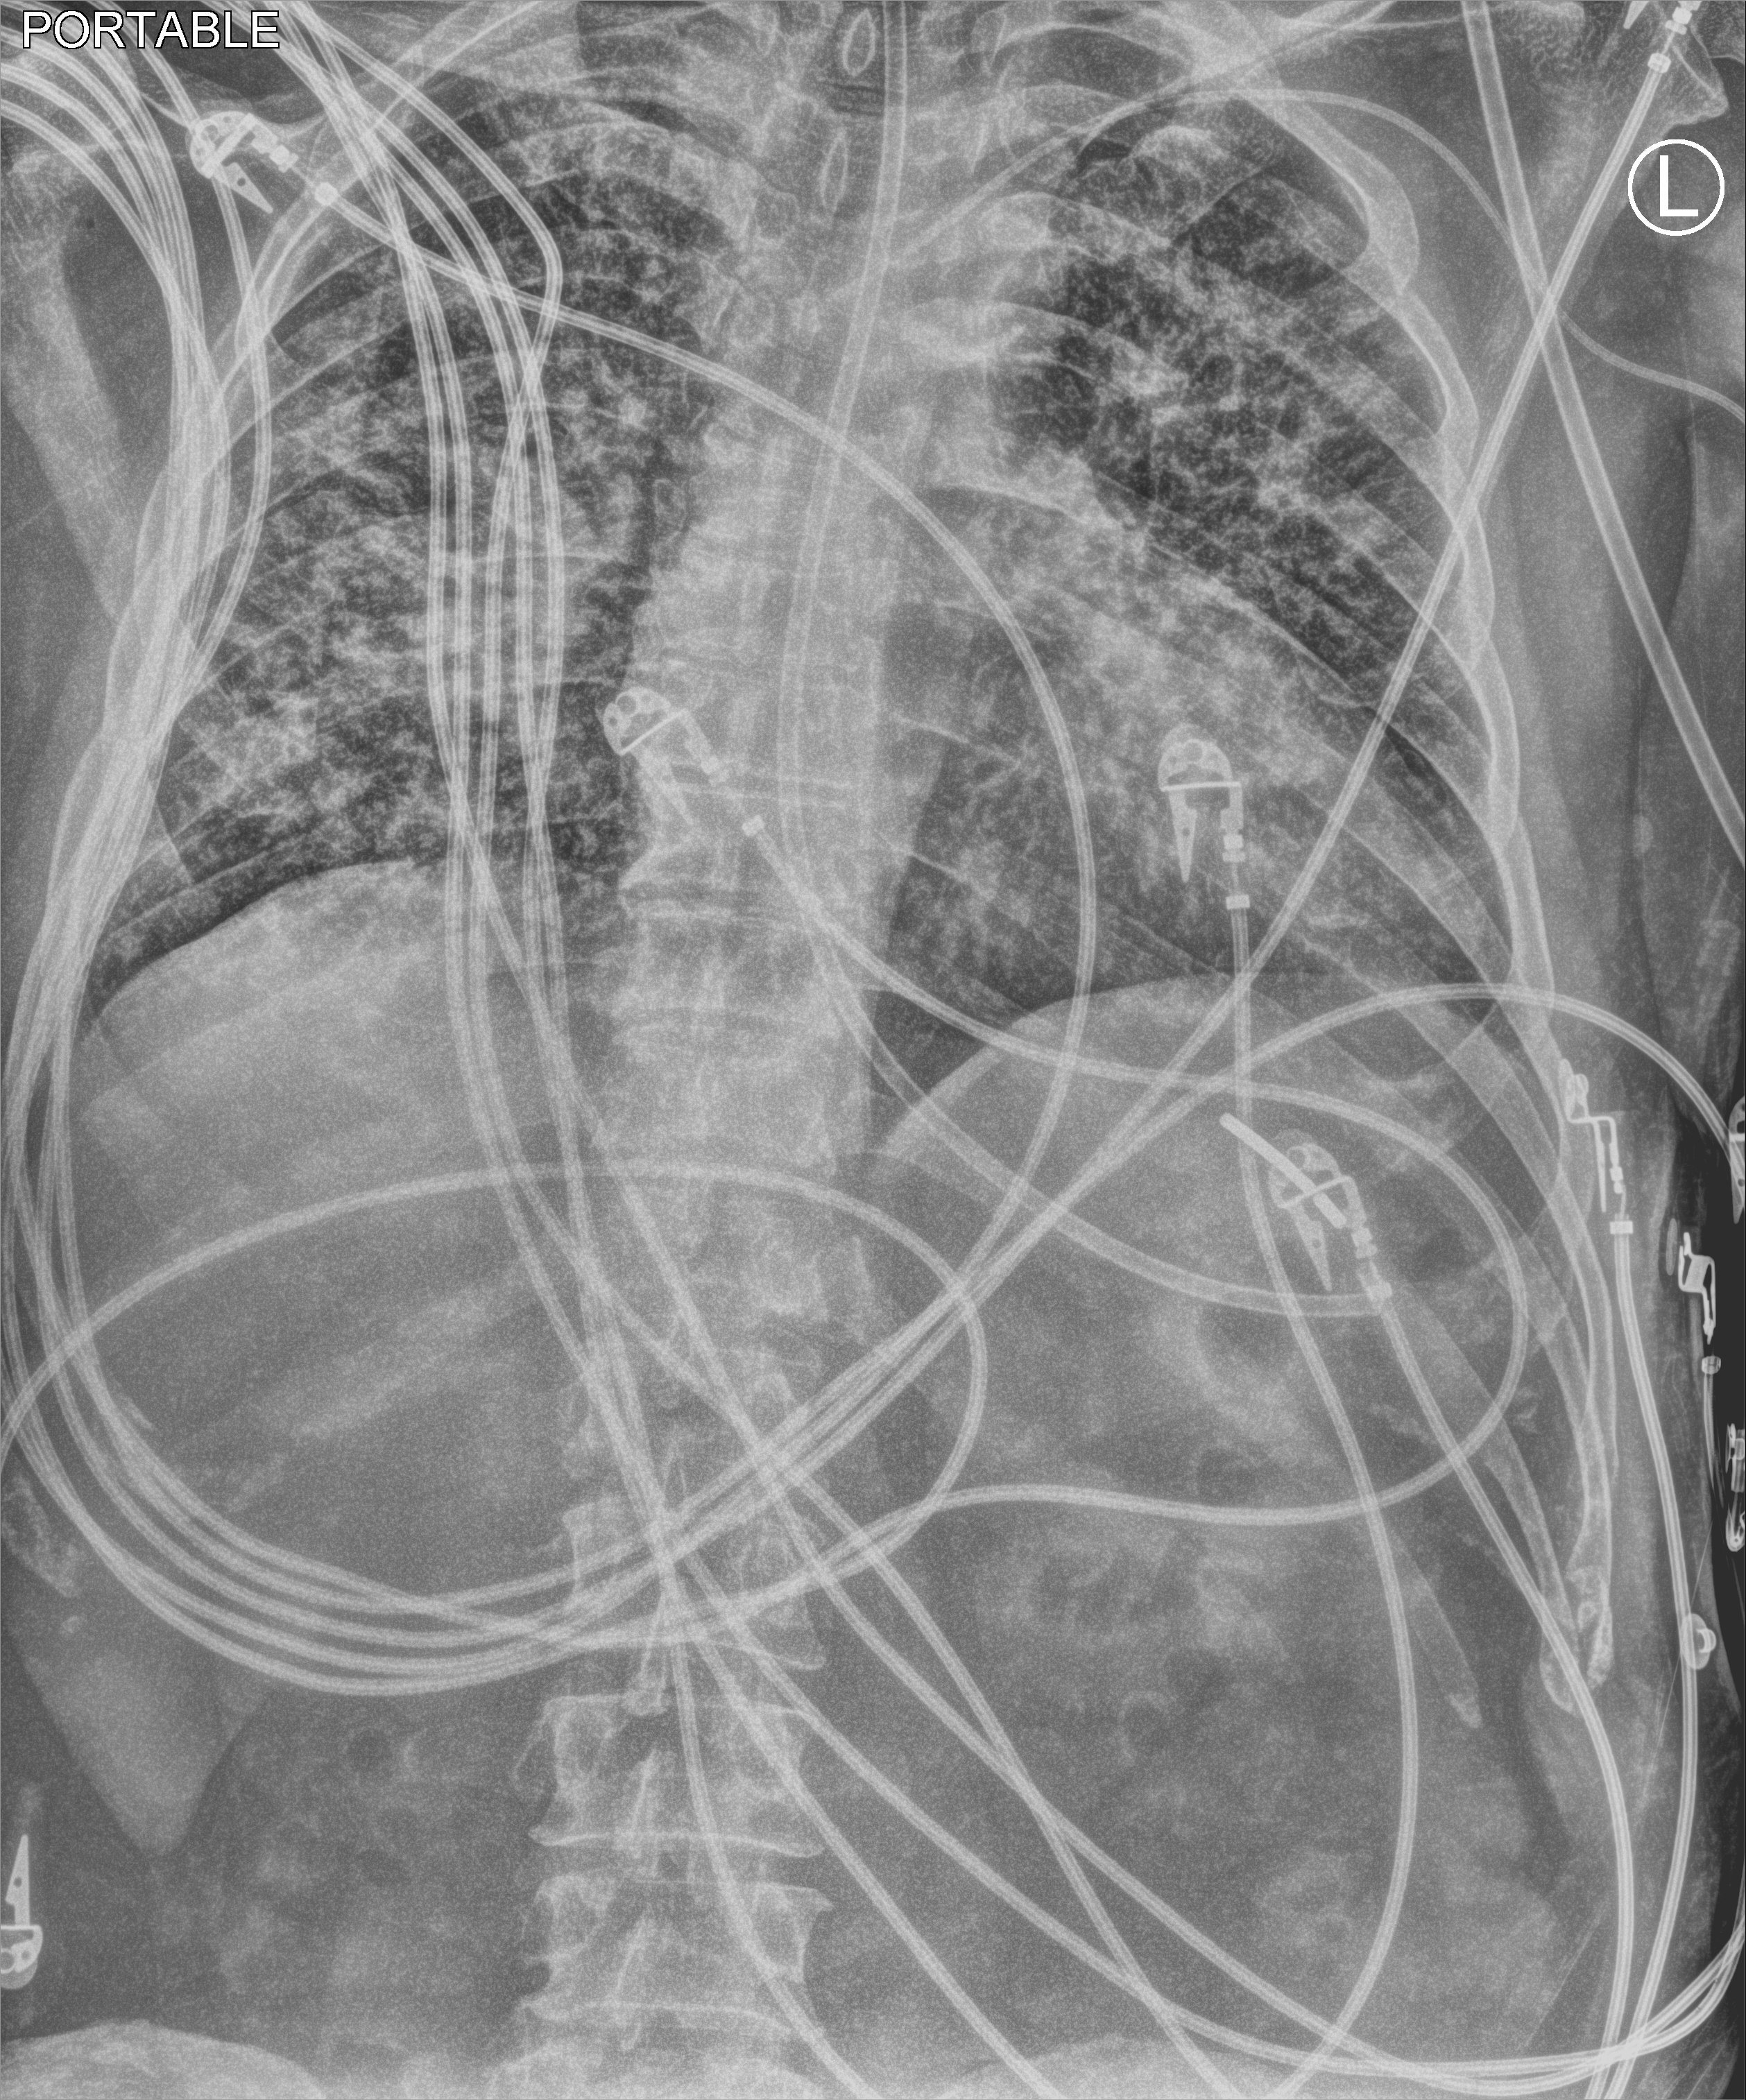
Portable chest radiograph; anteroposterior (AP) projection. Male patient hospitalised with COVID-19, age 18–59 years.
From the hospital-stay record, not from the radiograph (when in the stay this image was taken is not recorded):
- mechanically ventilated during this hospital stay: yes
- admitted to intensive care during this hospital stay: yes
- COPD (admission record): no